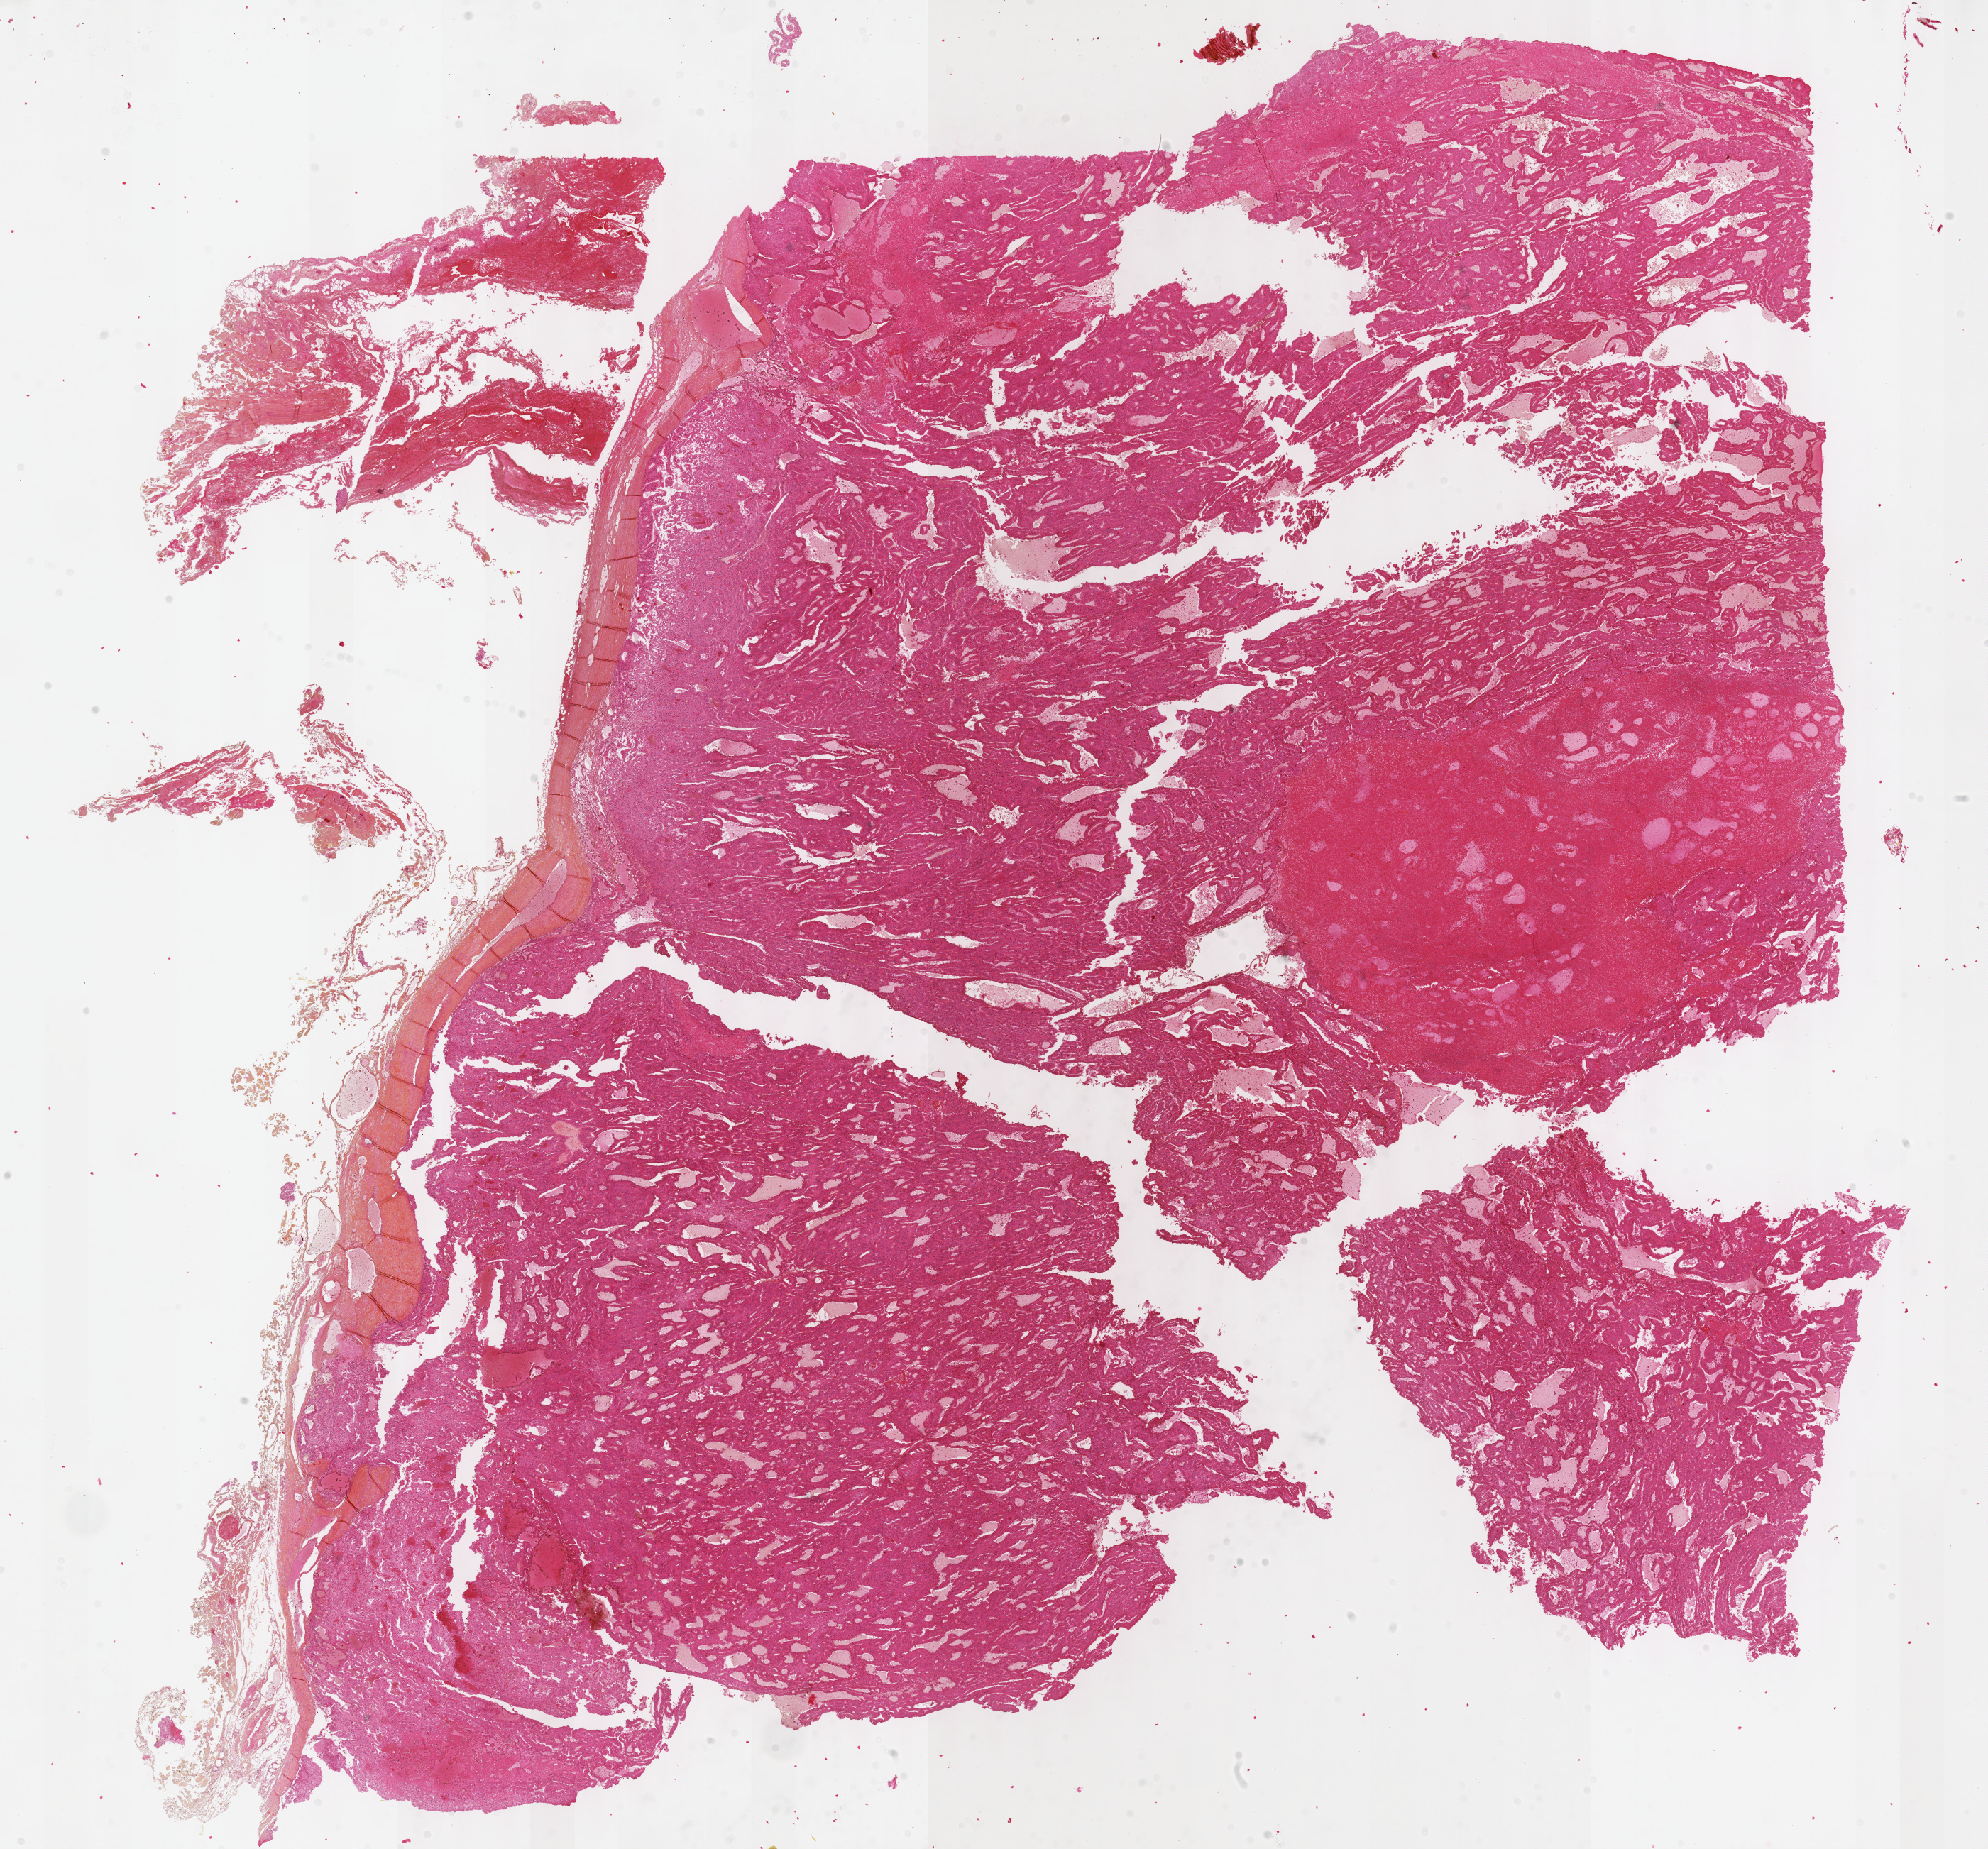
Whole-slide histology image, H&E, a low-resolution overview of the entire scanned area, about 22.6 x 21.1 mm (from a 40x scan), formalin-fixed paraffin-embedded (FFPE) diagnostic section, sample: primary tumour, adrenal cortex. Female, age 34 years at initial diagnosis.
Diagnosis: Adrenal cortical carcinoma (cortex of adrenal gland).